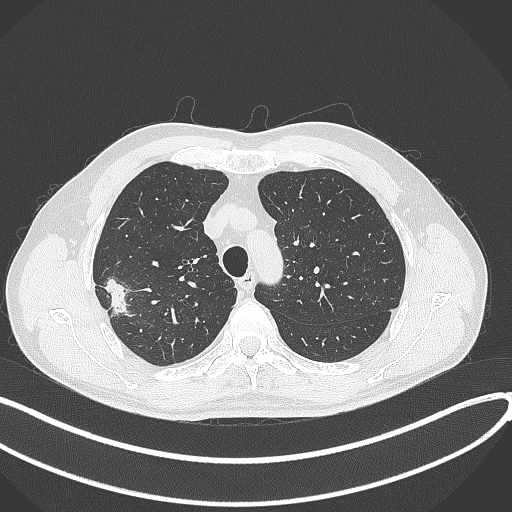
Chest CT, one axial slice. Position 322 of 381 along the scan axis. Lung window (W 1500 / L -600 HU). 512 × 512 image matrix, field of view 400 × 400 mm. Male patient, age 62 years. From the clinical record (not read from this slice): clinical TNM (as recorded): T1c N0 M0; histopathological grade: G2-3.
Outlined on this slice (rectangle marked by the reading radiologist):
- lung tumour (recorded histology: adenocarcinoma): box from (x=101, y=278) to (x=130, y=318) px